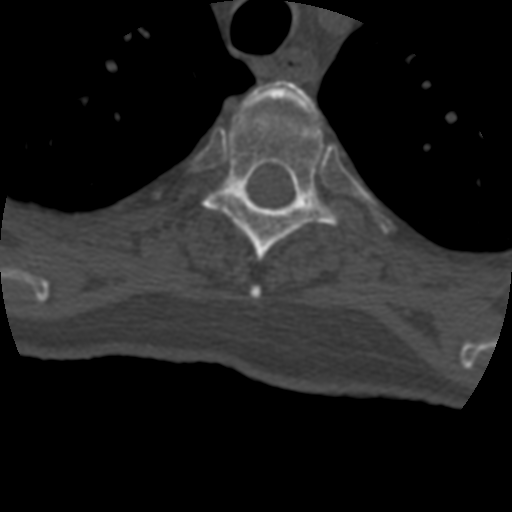
CT including the spine, one axial slice; slice 338 of 399 in the series (ordered by position); reconstruction kernel STANDARD; bone window (W 1800 / L 400 HU); 512 × 512 image matrix, field of view 160 × 160 mm. Patient age 69 years. From the clinical record (not read from this slice): primary cancer: prostate.
Structures marked on this image (semi-automatic segmentation, software-assisted and operator-edited):
- T3 vertebra: bounding box (x1, y1, x2, y2) in pixels: (239, 80, 316, 297)
- T4 vertebra: (182, 106, 364, 262)